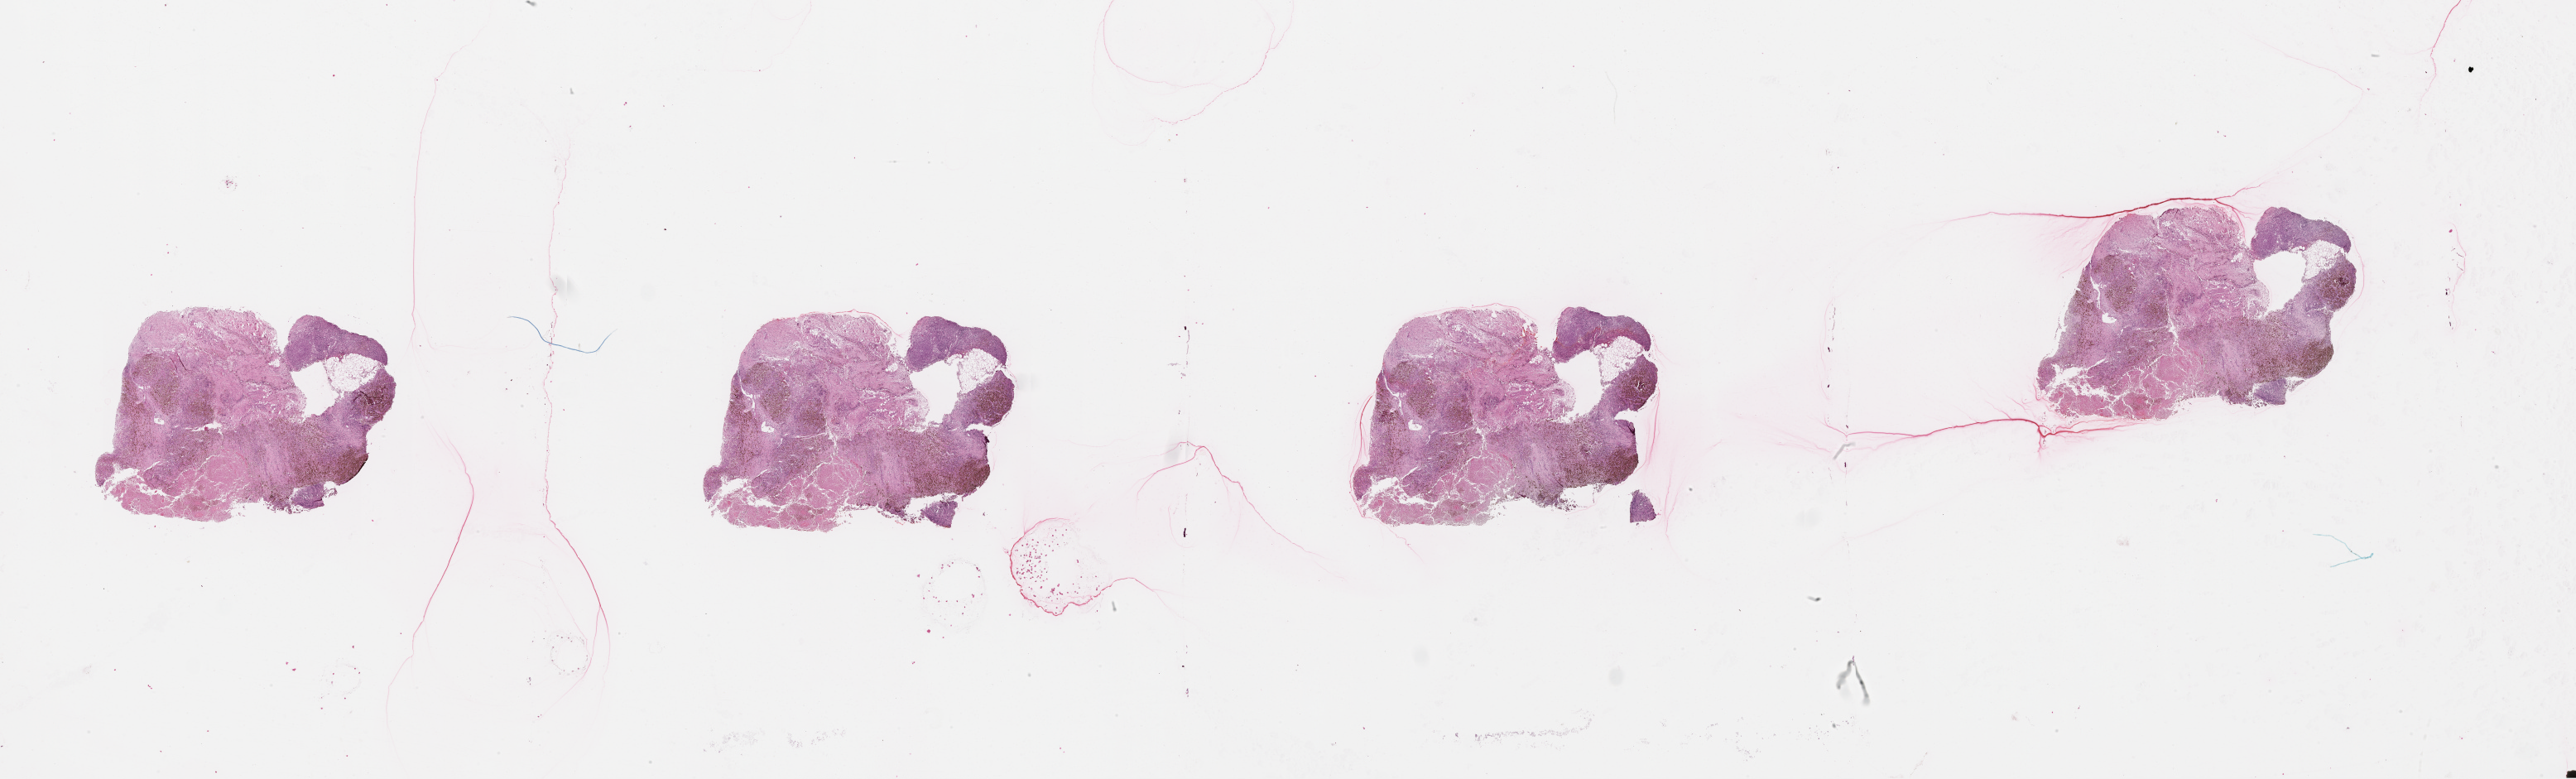
Whole-slide histology image, H&E-stained, a low-resolution overview of the entire scanned area, about 50.1 x 15.2 mm. Patient: male, age 87 years.
Patient diagnosis: Malignant melanoma, NOS.